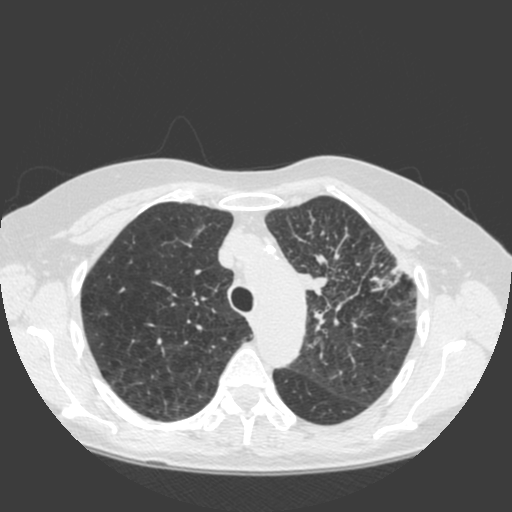
Low-dose screening chest CT, axial slice, first (baseline) screen, lung window (W 1500 / L -600 HU), 120 kVp, slice 42 of 184 in the series, 512 × 512 image matrix. Female participant, aged 66 years at enrolment. Current smoker at enrolment.
Lesion marked by an expert reader, bounding box <287,249,396,346> (left, top, right, bottom; pixels). Screening reader's record for this exam (one nodule recorded; not confirmed to be the boxed lesion): non-calcified nodule or mass ≥4 mm, left upper lobe, 61 × 45 mm, spiculated (stellate) margins, soft tissue attenuation. Official screen result: positive, change unspecified: nodule(s) >= 4 mm or enlarging nodule(s), mass(es), or other non-specific abnormalities suspicious for lung cancer. Participant outcome: lung cancer diagnosed 19 days after this screen — squamous cell carcinoma, keratinizing, NOS, left upper lobe, left hilum, mediastinum, left main stem bronchus, other location, poorly differentiated (G3), stage IIIB (AJCC 6th edition), 60 mm at pathology.